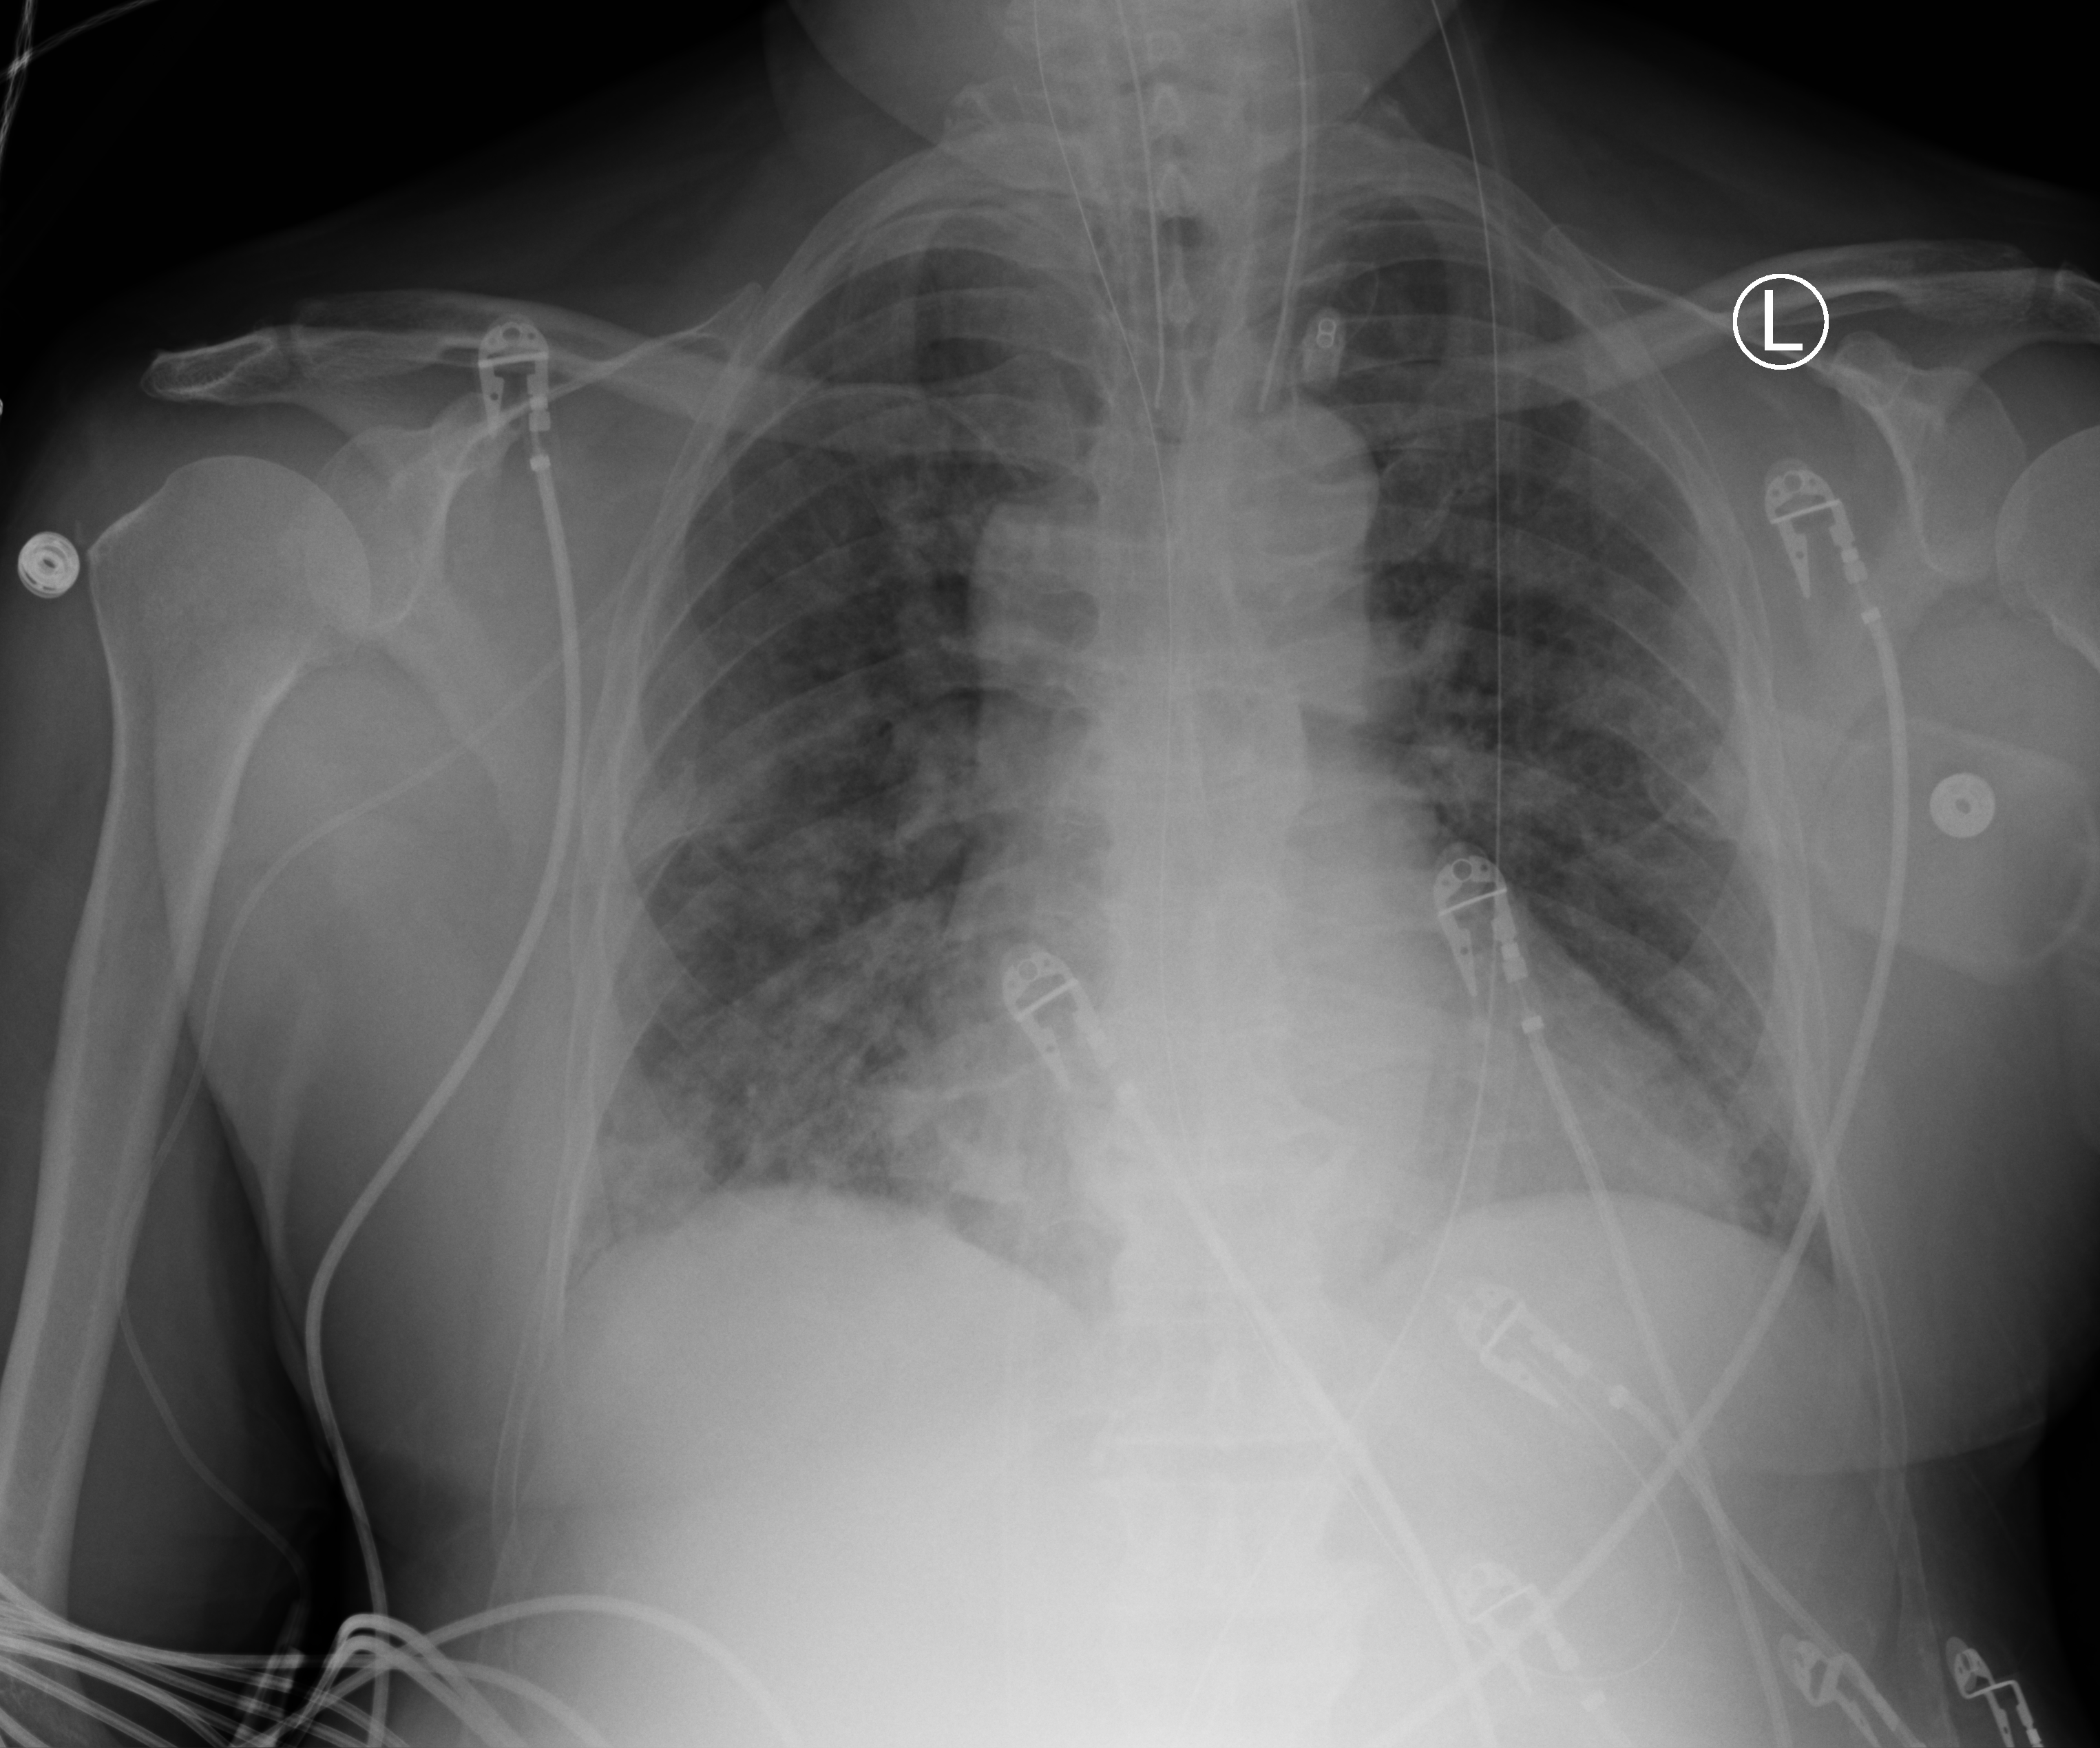
Chest X-ray (portable); anteroposterior (AP) projection. Patient hospitalised with COVID-19; male, aged 60–74 years.
Admission-level facts for this patient (not findings on this image; timing relative to this image not recorded):
- length of hospital stay: 31 days
- other chronic lung disease (admission record): yes